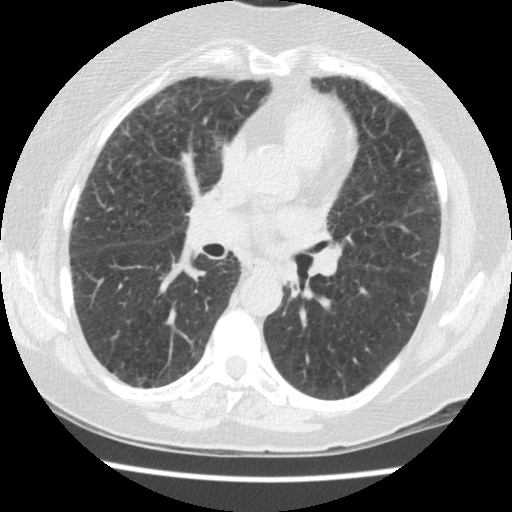
Chest CT (low-dose screening protocol), one axial image, second screening round (one year after baseline), lung window (W 1500 / L -600 HU), standard (soft-tissue) reconstruction kernel (STANDARD), slice 63 of 134 in the series, 512 × 512 image matrix, field of view 310 × 310 mm. Female participant, aged 60 years at enrolment.
• Expert-annotated lung lesion, bounding box <269,256,316,301> (left, top, right, bottom; pixels).
• The exam's reader record, not a measurement of the box and not confirmed to be the same lesion: non-calcified nodule or mass ≥4 mm, left lower lobe, 5 × 4 mm, smooth margins, soft tissue attenuation, pre-existing on the prior screen: yes; interval growth: no.